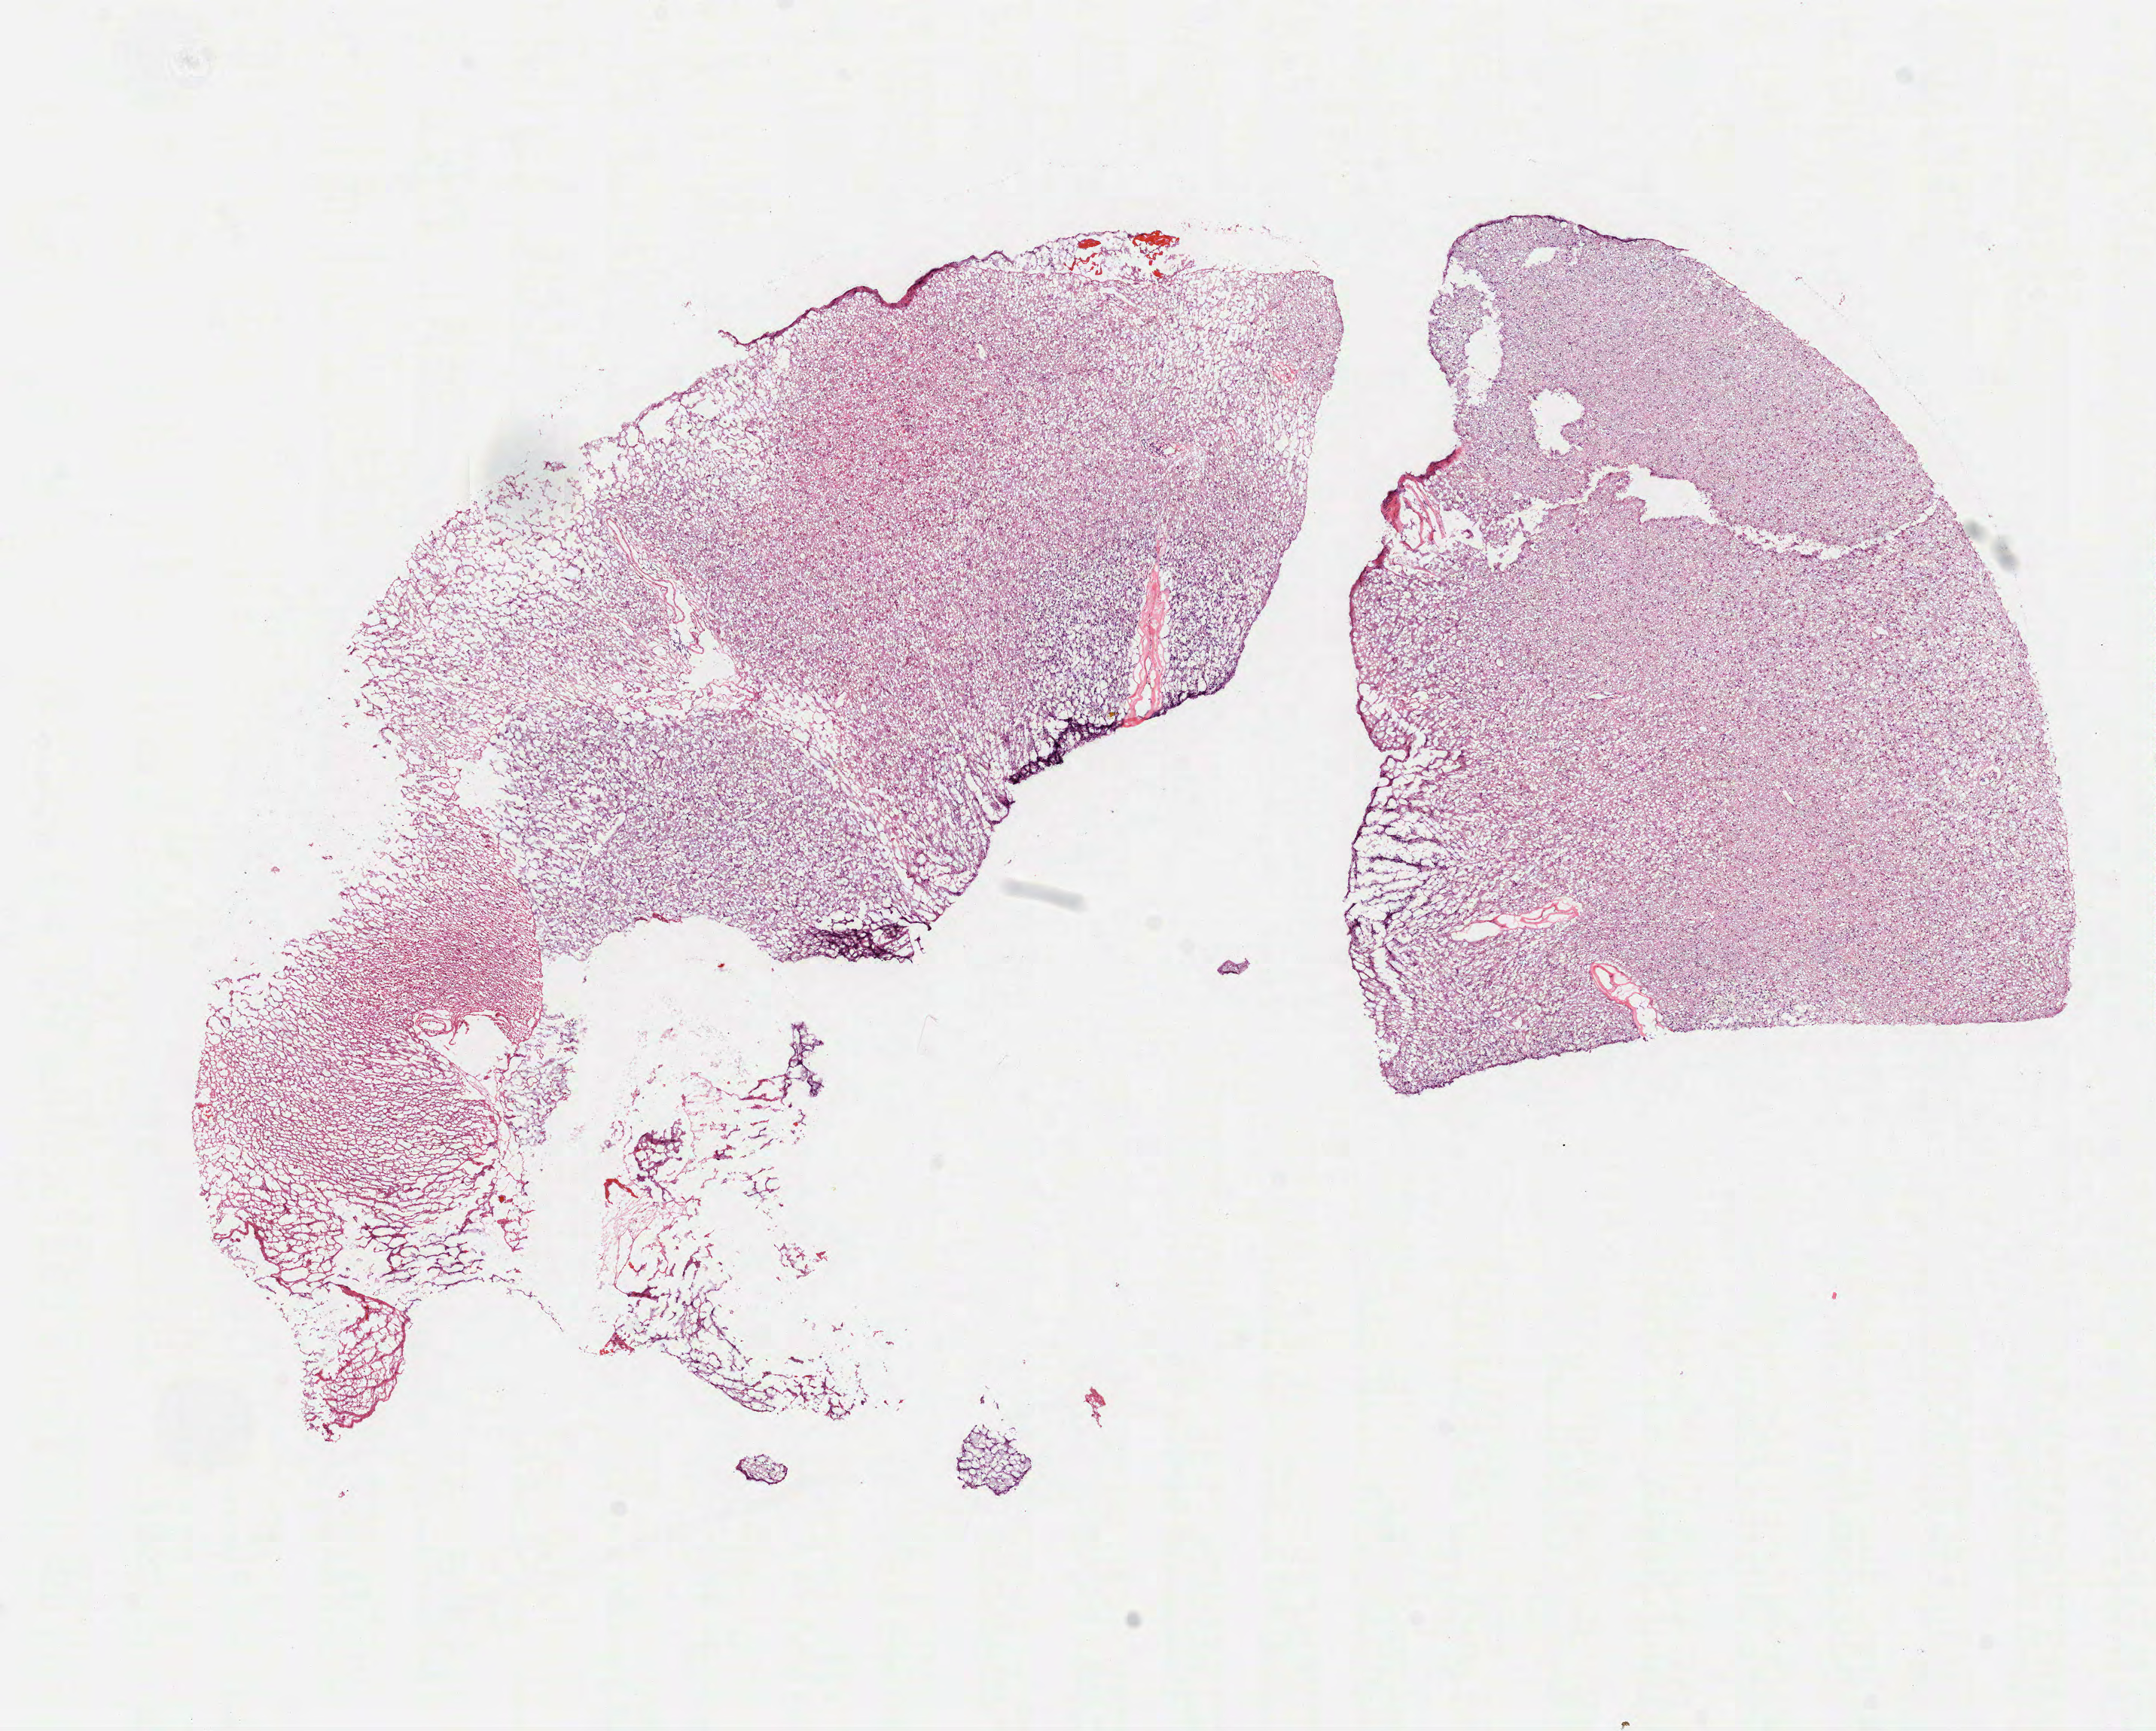
Digitized Hematoxylin and eosin (H&E) stained tissue section (whole slide), a low-resolution overview of the entire scanned area, about 11.5 x 9.3 mm (acquisition: 40x scan); frozen section; brain, primary tumour sample. Patient: male, age at initial diagnosis 54 years. Histologic grade: G3 (poorly differentiated). Slide review estimates, as recorded: tumour cells 100%, tumour nuclei 60%, normal cells 0%, stromal cells 0%, necrosis 0%.
Histologic diagnosis: Oligodendroglioma, anaplastic (cerebrum).